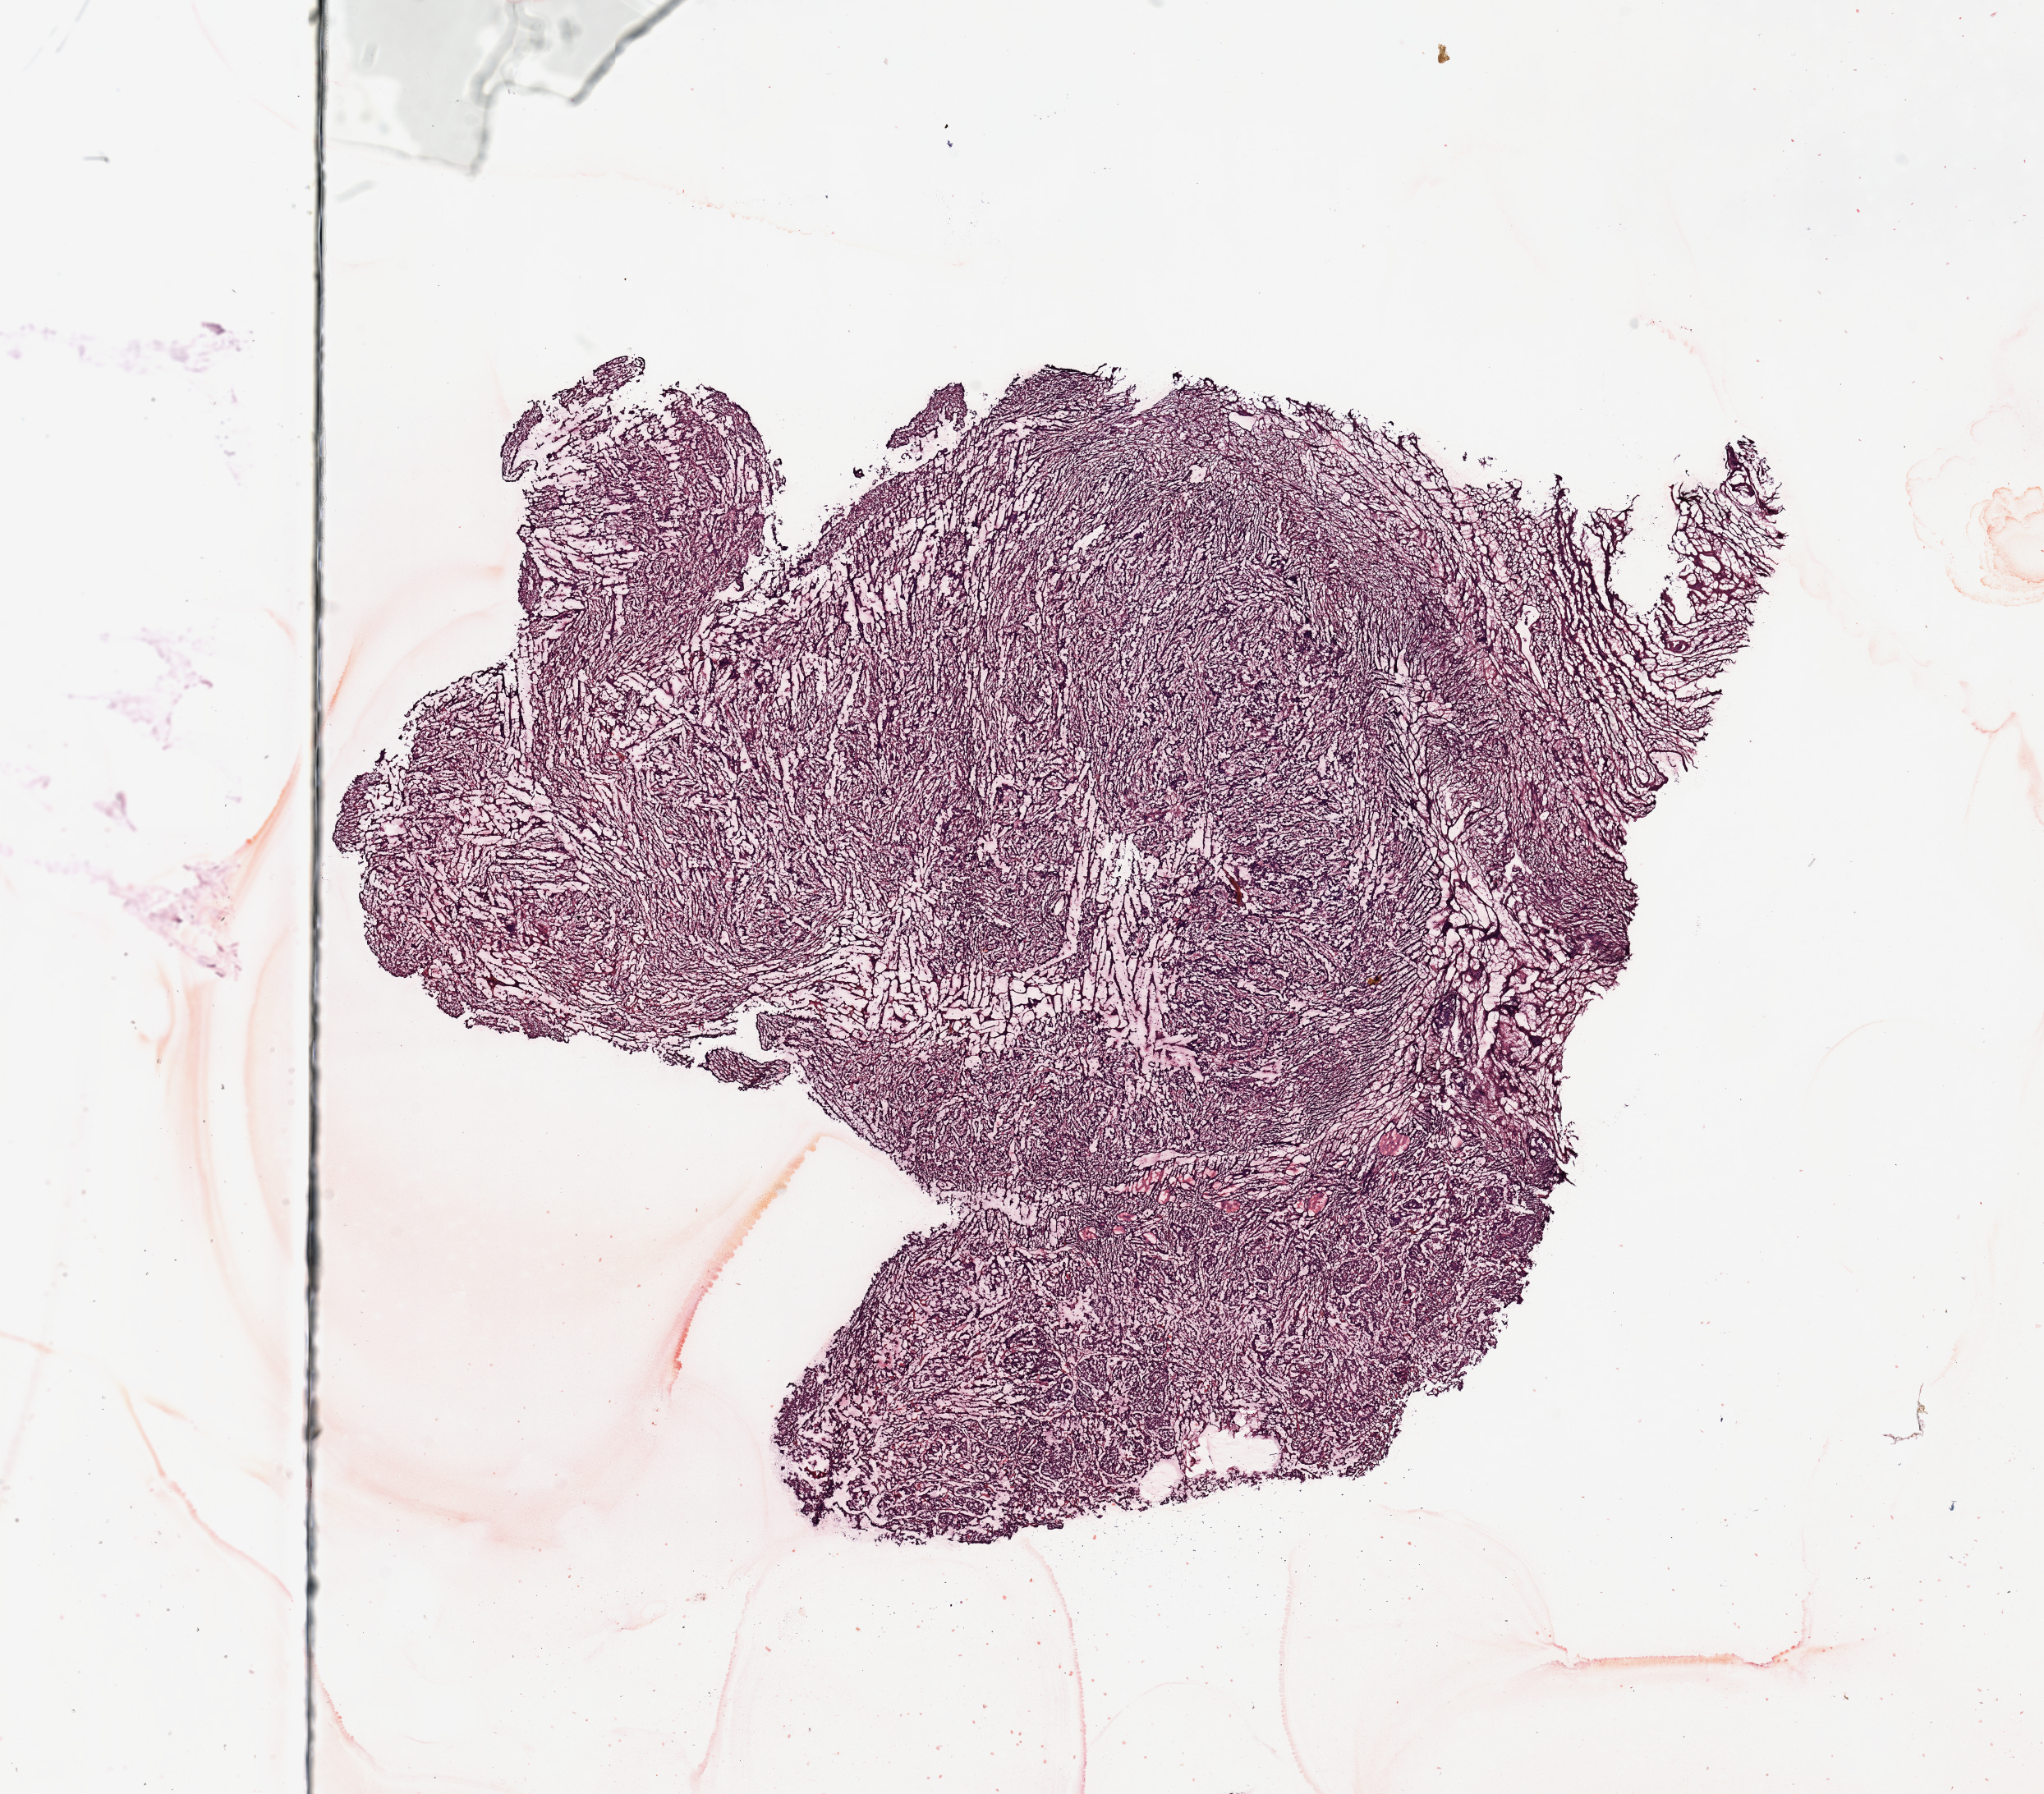
Whole-slide histology image, H&E-stained — whole scanned area (about 19.7 x 17.3 mm, from a 20x scan) shown as a low-resolution overview, uterus, tumour tissue. 75-year-old female patient.
Histologic diagnosis: Endometrioid adenocarcinoma, NOS.